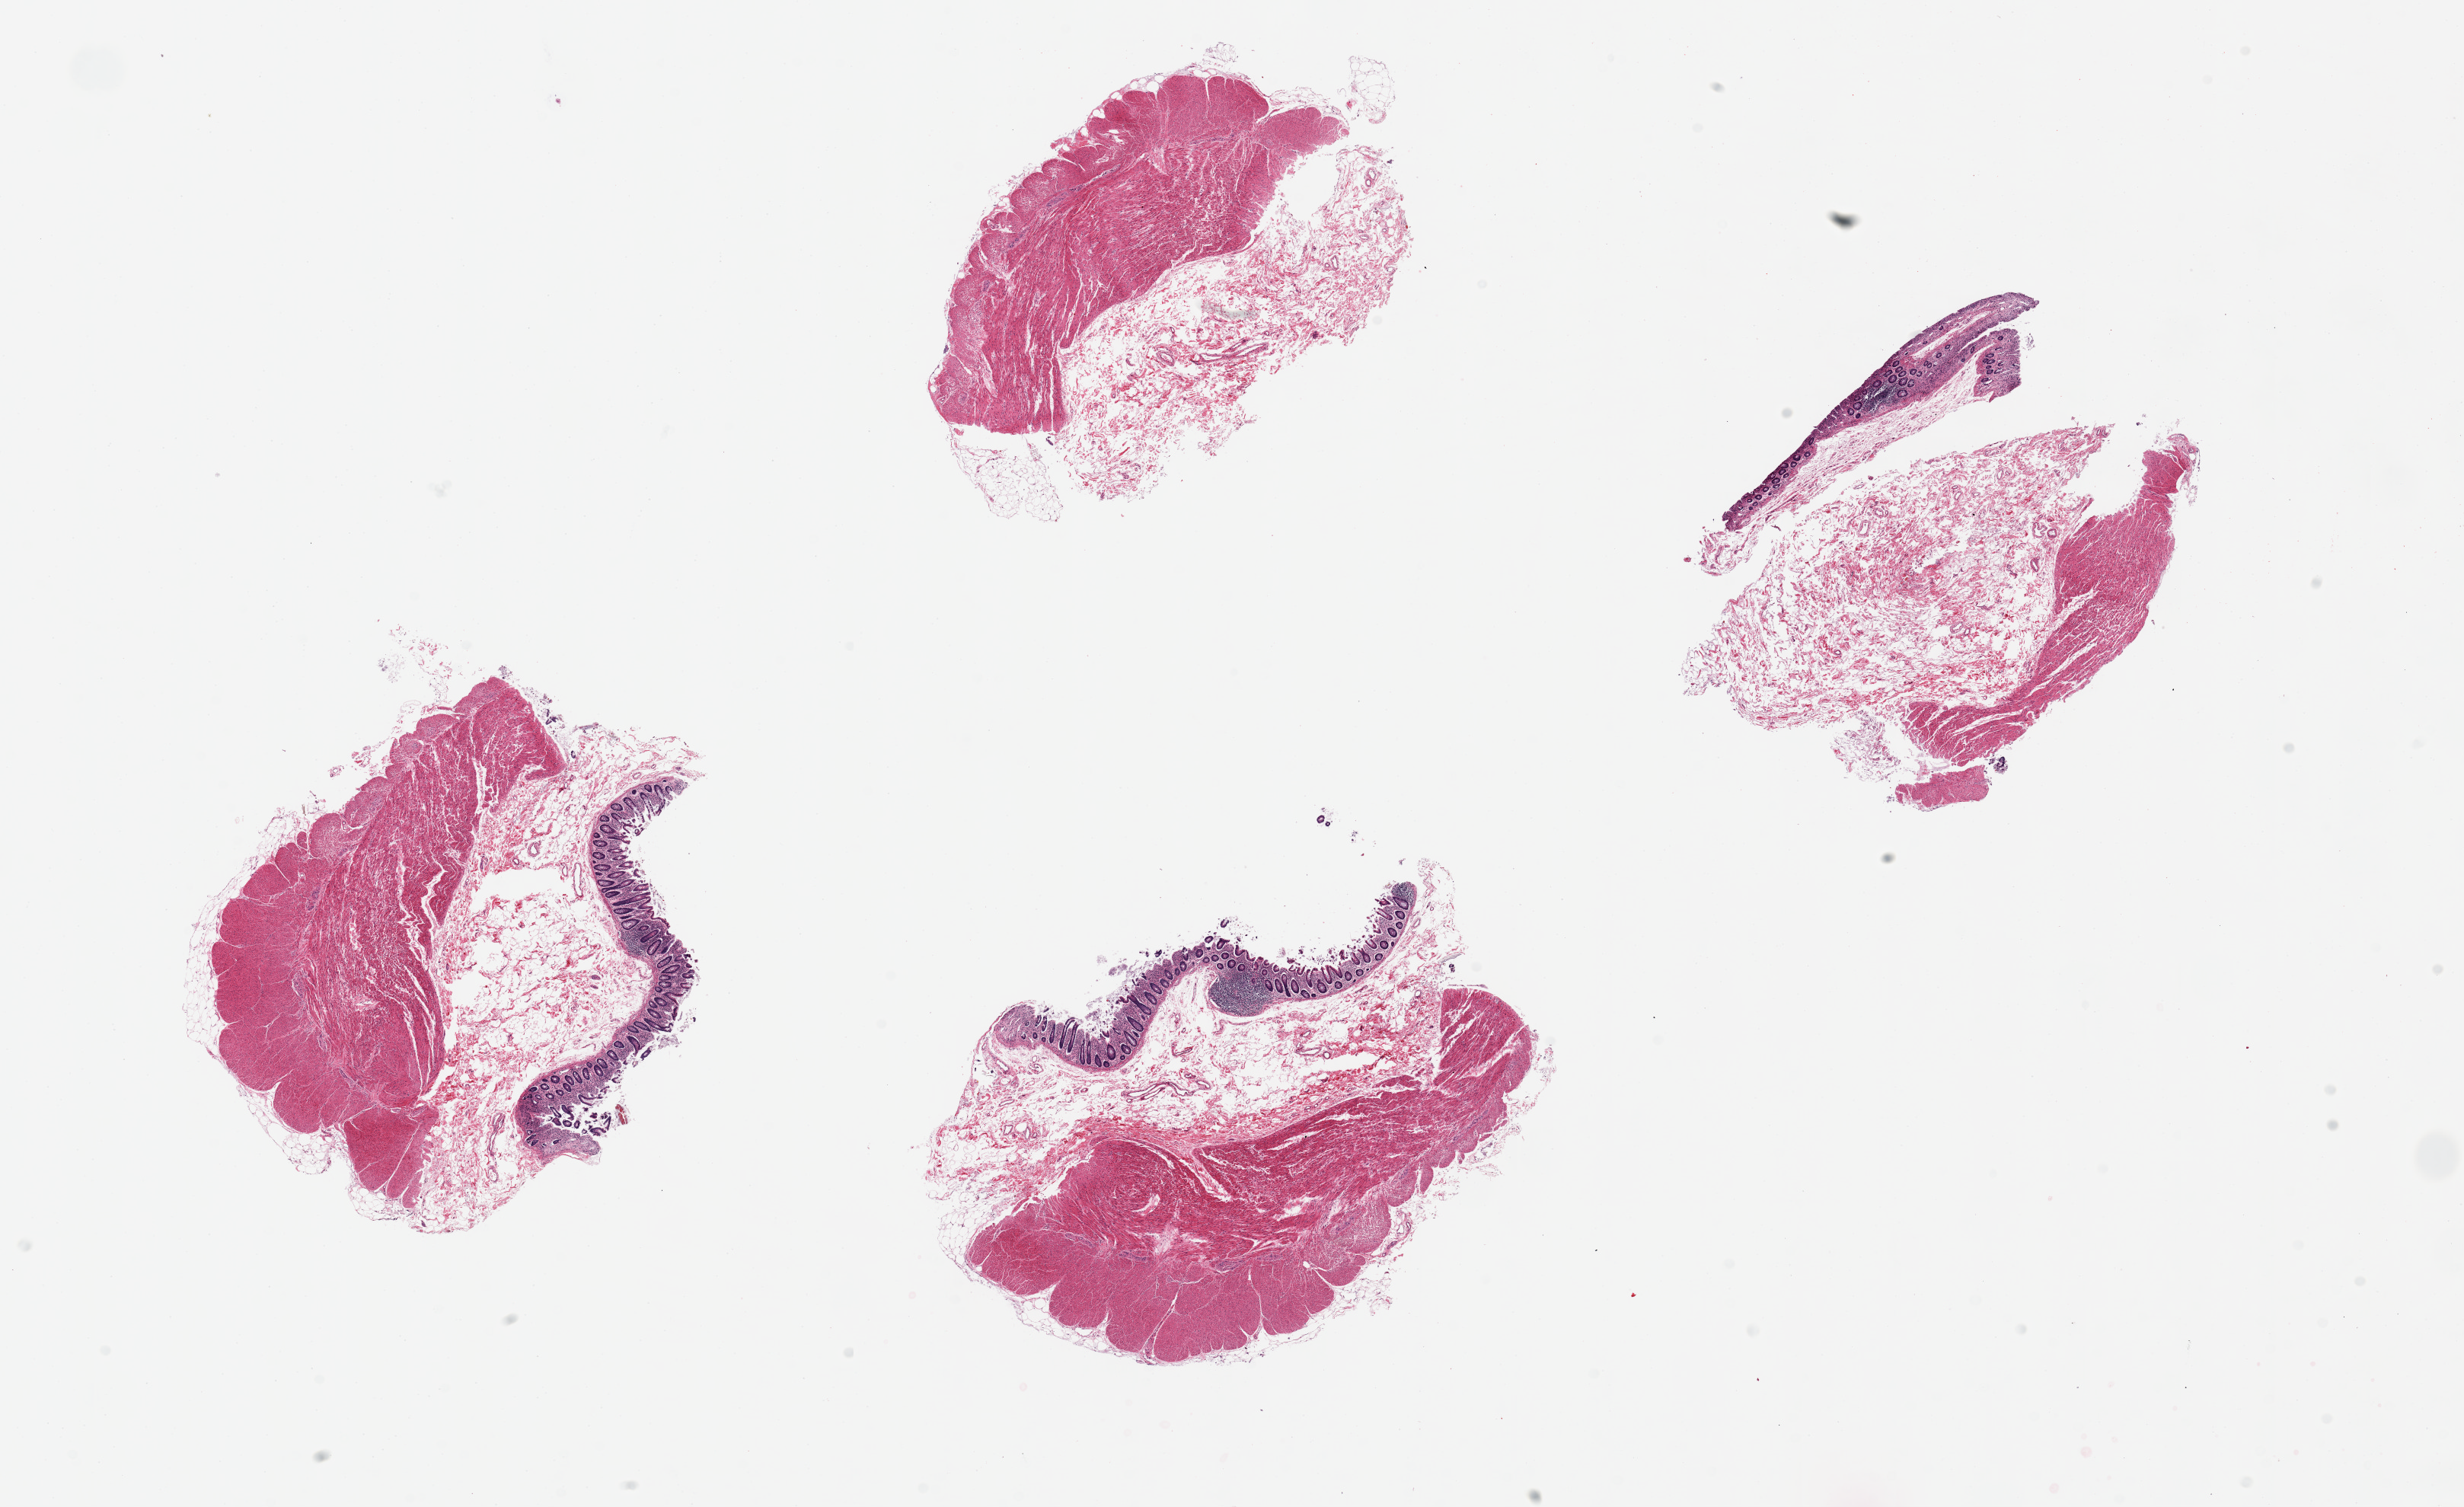
Digitized hematoxylin and eosin (H&E)-stained section, brightfield — whole scanned area (about 25.6 x 15.7 mm, acquisition: 20x scan) shown as a low-resolution overview, PAXgene-fixed, paraffin-embedded tissue, target tissue: sigmoid colon, tissue donor sample.
Review note (as recorded): 6 pieces ~6x3mm Only ~50% muscle delinieated, rest fat/mucosa.